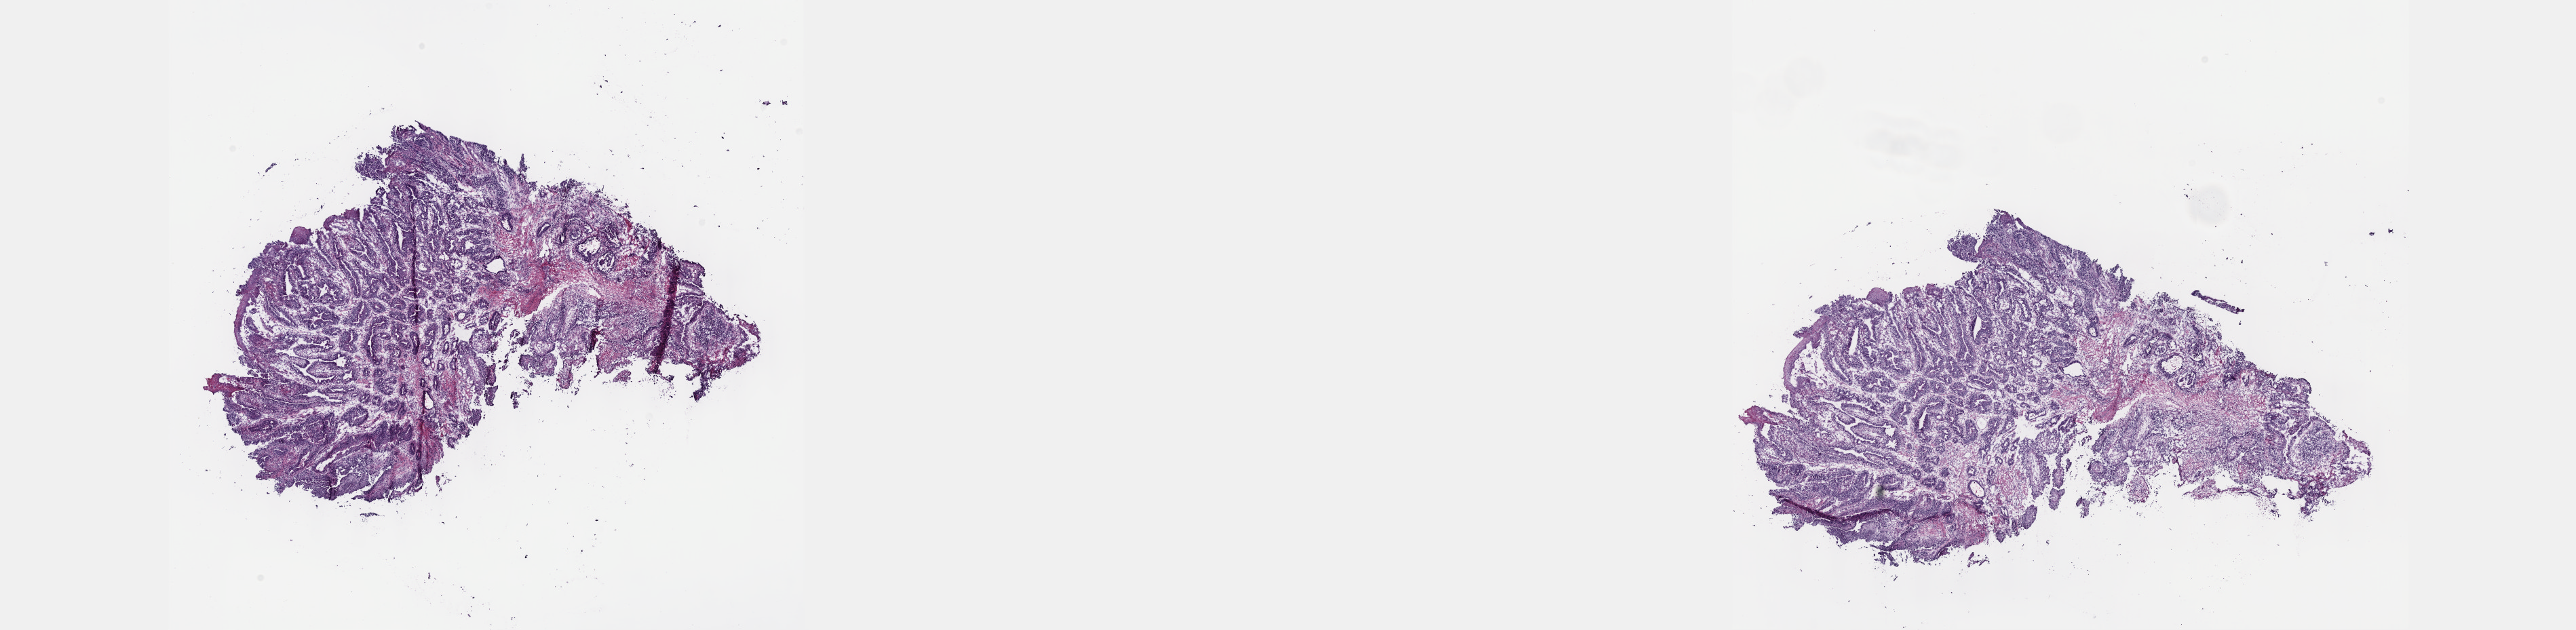
Digitized Hematoxylin and eosin (H&E) stained tissue section (whole slide), shown as a low-resolution overview of the whole scanned area (about 30.7 x 7.5 mm, slide scanned at 40x), frozen section from the top of the tissue portion, primary tumour sample from the esophagus. Male, age 53 years at initial diagnosis. Histologic grade: G2 (moderately differentiated). Slide review estimates, as recorded: tumour cells 48%, tumour nuclei 75%, normal cells 6%, stromal cells 43%, necrosis 3%. Inflammatory infiltration, as recorded: lymphocyte infiltration 12%, monocyte infiltration 2%, neutrophil infiltration 2%.
Pathologic diagnosis: Adenocarcinoma, NOS (lower third of esophagus). TNM: T1 N1 M0. AJCC pathologic stage: IIB.